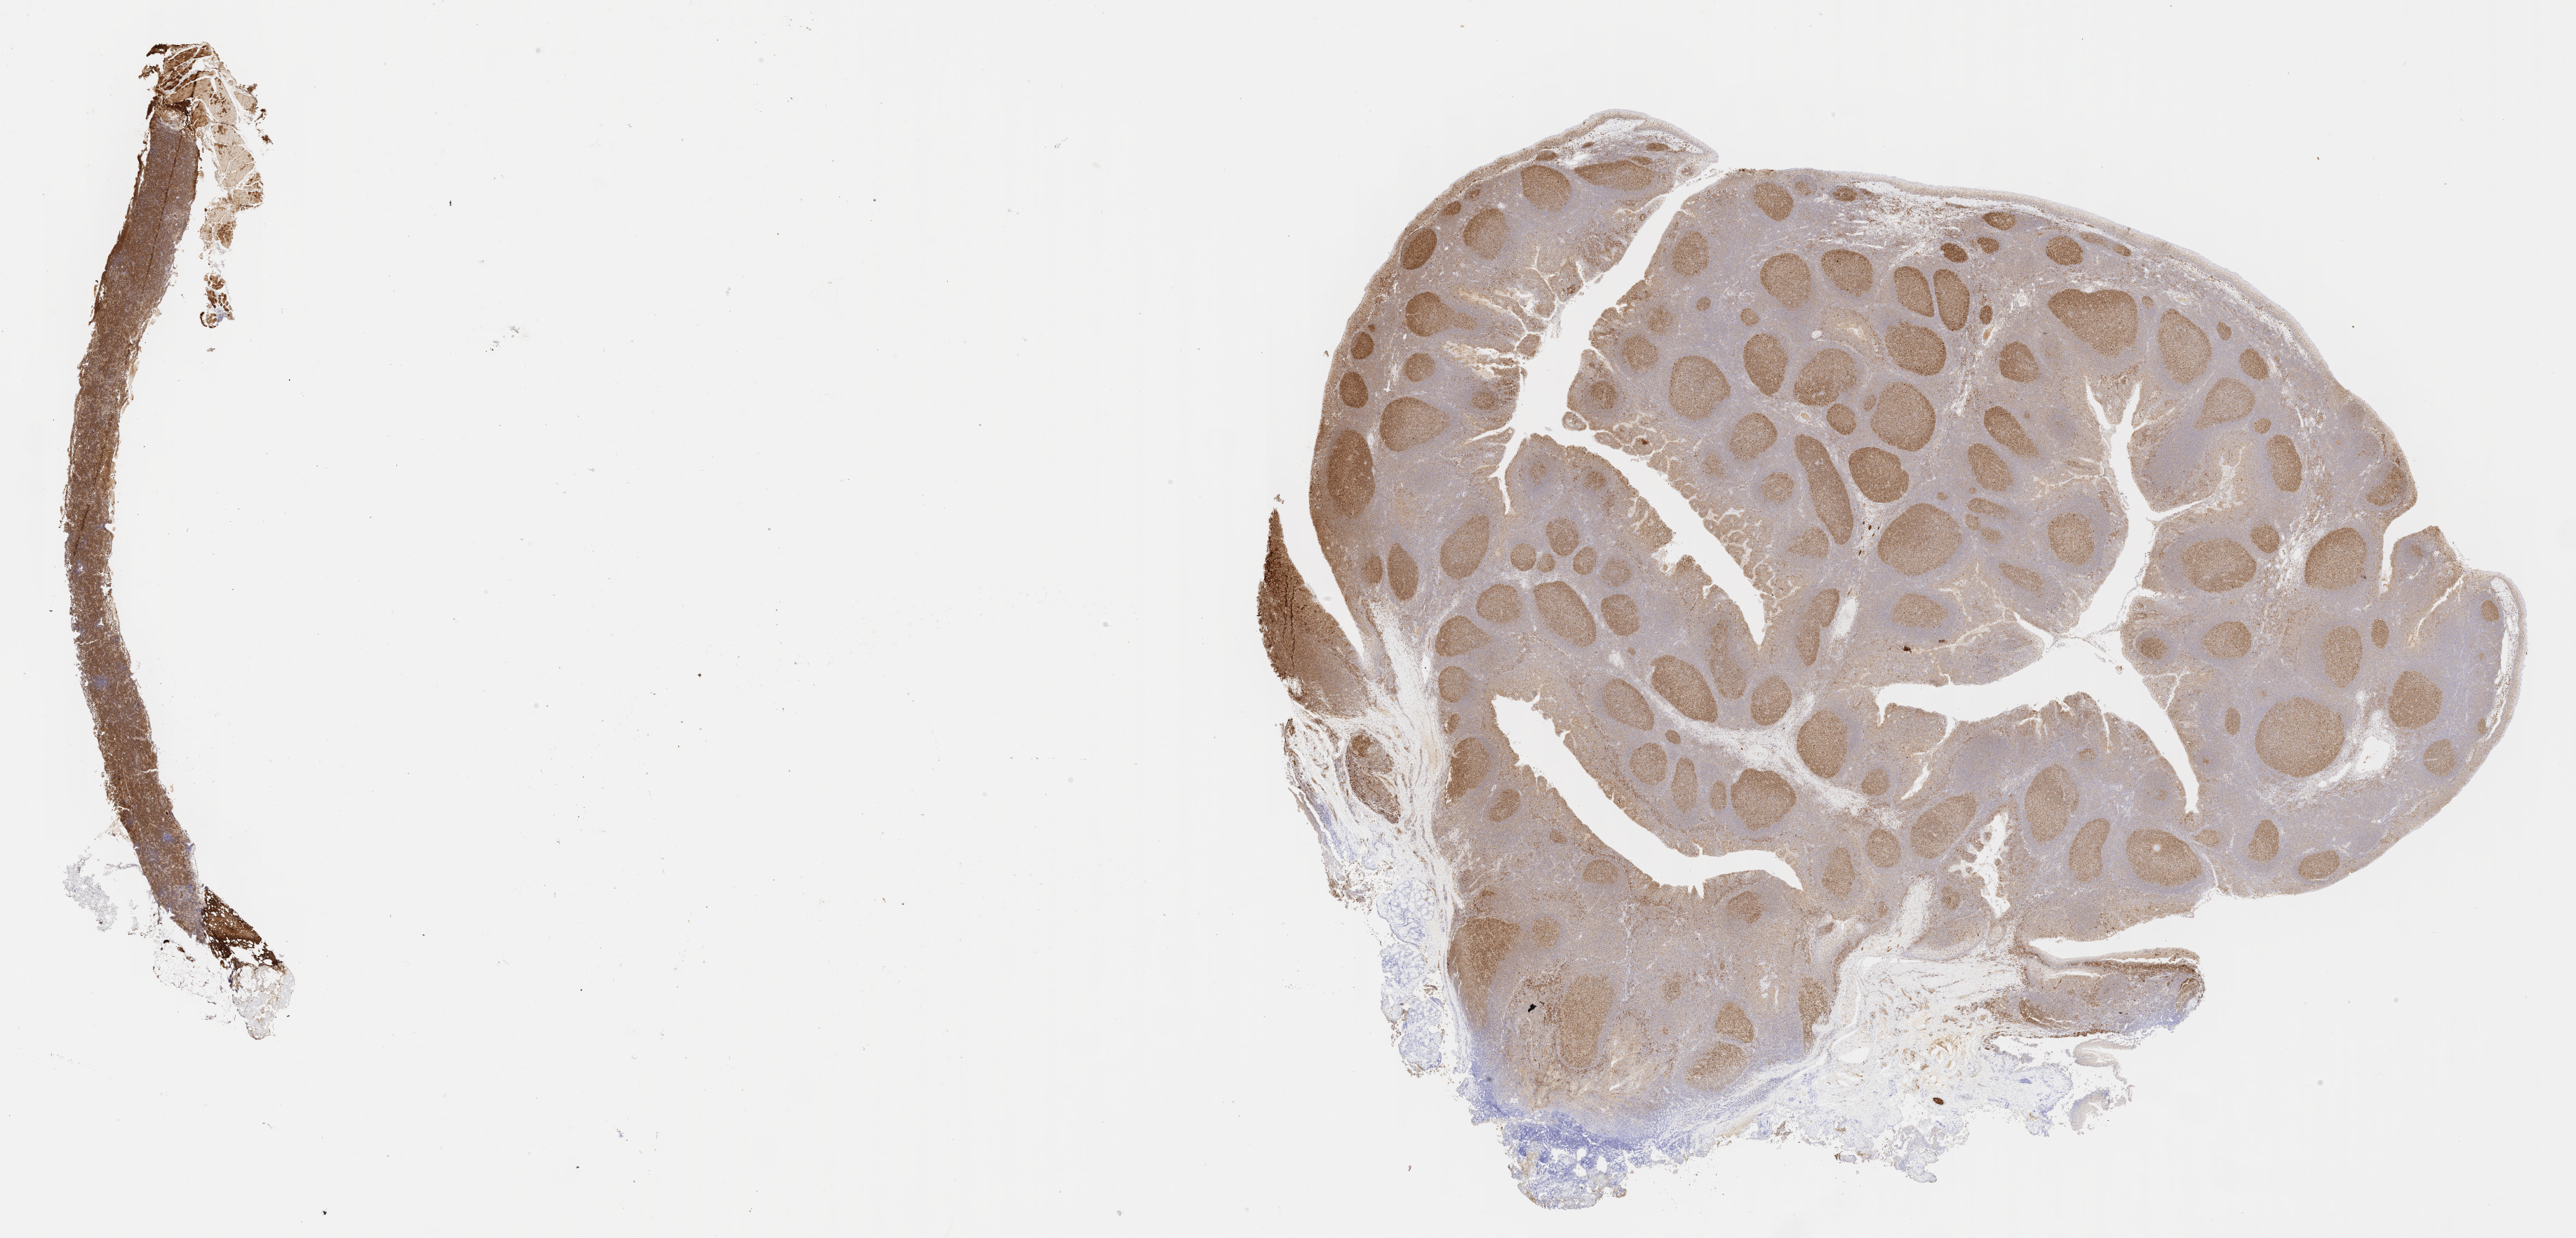
Whole-slide image, immunohistochemical stain for BCL6, shown as a low-resolution overview of the whole scanned area (about 29.7 x 14.3 mm), tumor tissue, site: cranium. Female patient; age at initial diagnosis 7 years.
Diagnosis: Burkitt lymphoma, NOS.